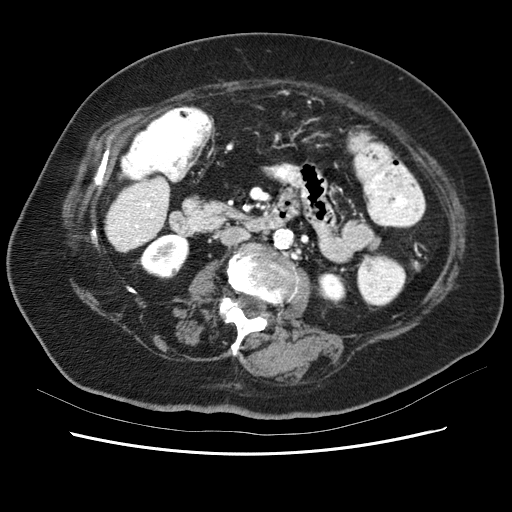
Contrast-enhanced abdominal CT (liver protocol), one axial slice; slice 11 of 62 in the series (ordered by position); reconstruction kernel STANDARD; soft-tissue window (W 400 / L 40 HU); 2.5 mm slice thickness; 512 × 512 image matrix. From the clinical record (not read from this slice): diagnosis: hepatocellular carcinoma (patient treated with transarterial chemoembolisation; whether this scan precedes or follows treatment is not stated here); TNM stage (as recorded): Stage-I; Child-Pugh class: B; tumour nodularity: uninodular.
Outlined on this slice (semi-automatic segmentation, software-assisted and operator-edited):
- liver parenchyma outside the tumour (the mass and vessels are separate outlines, so this box may not span the whole liver): box from (x=102, y=176) to (x=168, y=254) px
- liver vessels: (x=108, y=178)–(x=165, y=251)